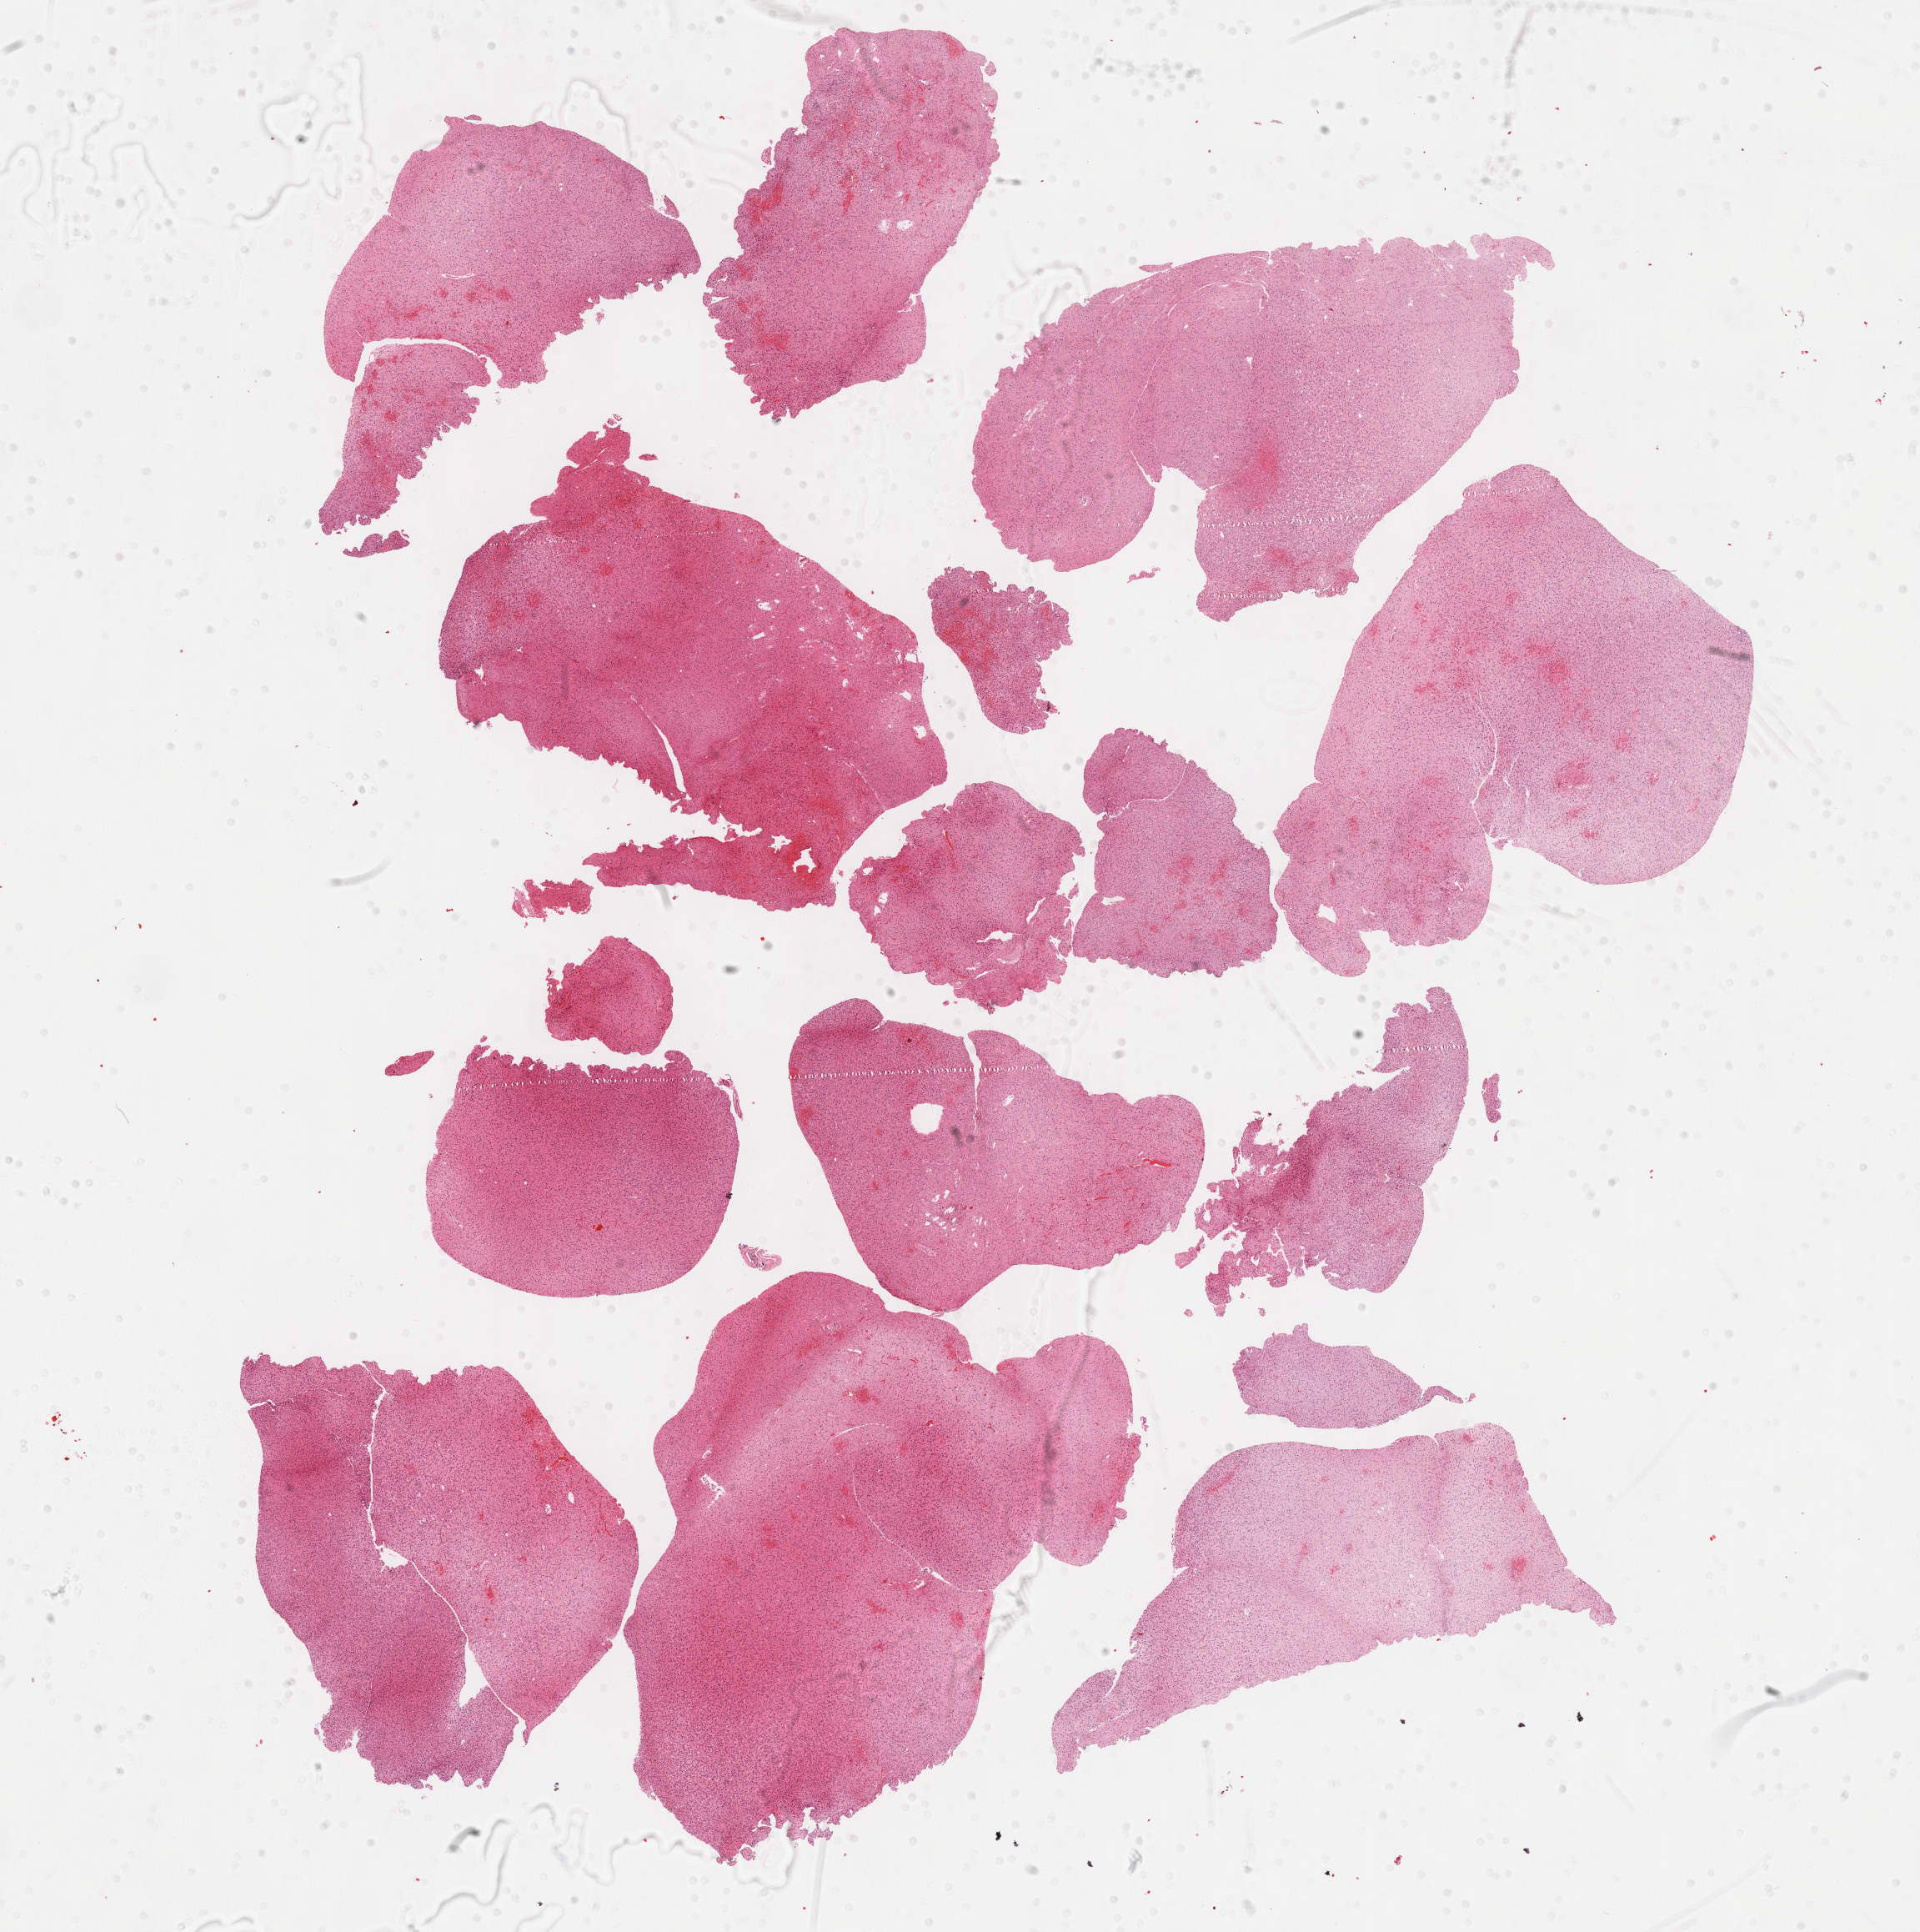
H&E-stained whole-slide image, a low-resolution overview of the entire scanned area, about 18.6 x 18.7 mm. FFPE section. Primary tumour sample from the brain. Patient: female, age at initial diagnosis 38 years. Histologic grade: G3 (poorly differentiated).
Laterality: left. Histologic diagnosis: Astrocytoma, anaplastic (cerebrum).